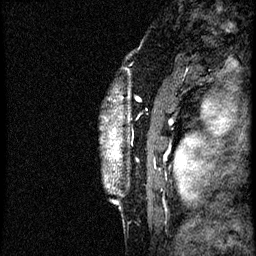
Breast MRI (dynamic contrast-enhanced), one sagittal slice; dynamic contrast-enhanced study with each time point stored as its own series, time point 2 of 3 at this slice position (early post-contrast, ordered by acquisition time); 1.5 T; TE 4.2 ms, TR 21.3 ms; 256 × 256 image matrix, field of view 200 × 200 mm. Patient: female, 41 years. Case-level facts recorded for this patient, not image findings: setting: breast cancer imaged before/during neoadjuvant chemotherapy; receptor status: HER2-positive.
Structures marked on this image (semi-automatically segmented with operator editing):
- analysis volume of interest (the breast-tissue region the enhancement analysis was run in; not a lesion): bounding box <100,84,177,205> (left, top, right, bottom; pixels)
- tumour enhancement mask (voxels above the 100 % enhancement threshold inside the analysis volume of interest): <111,131,119,158>